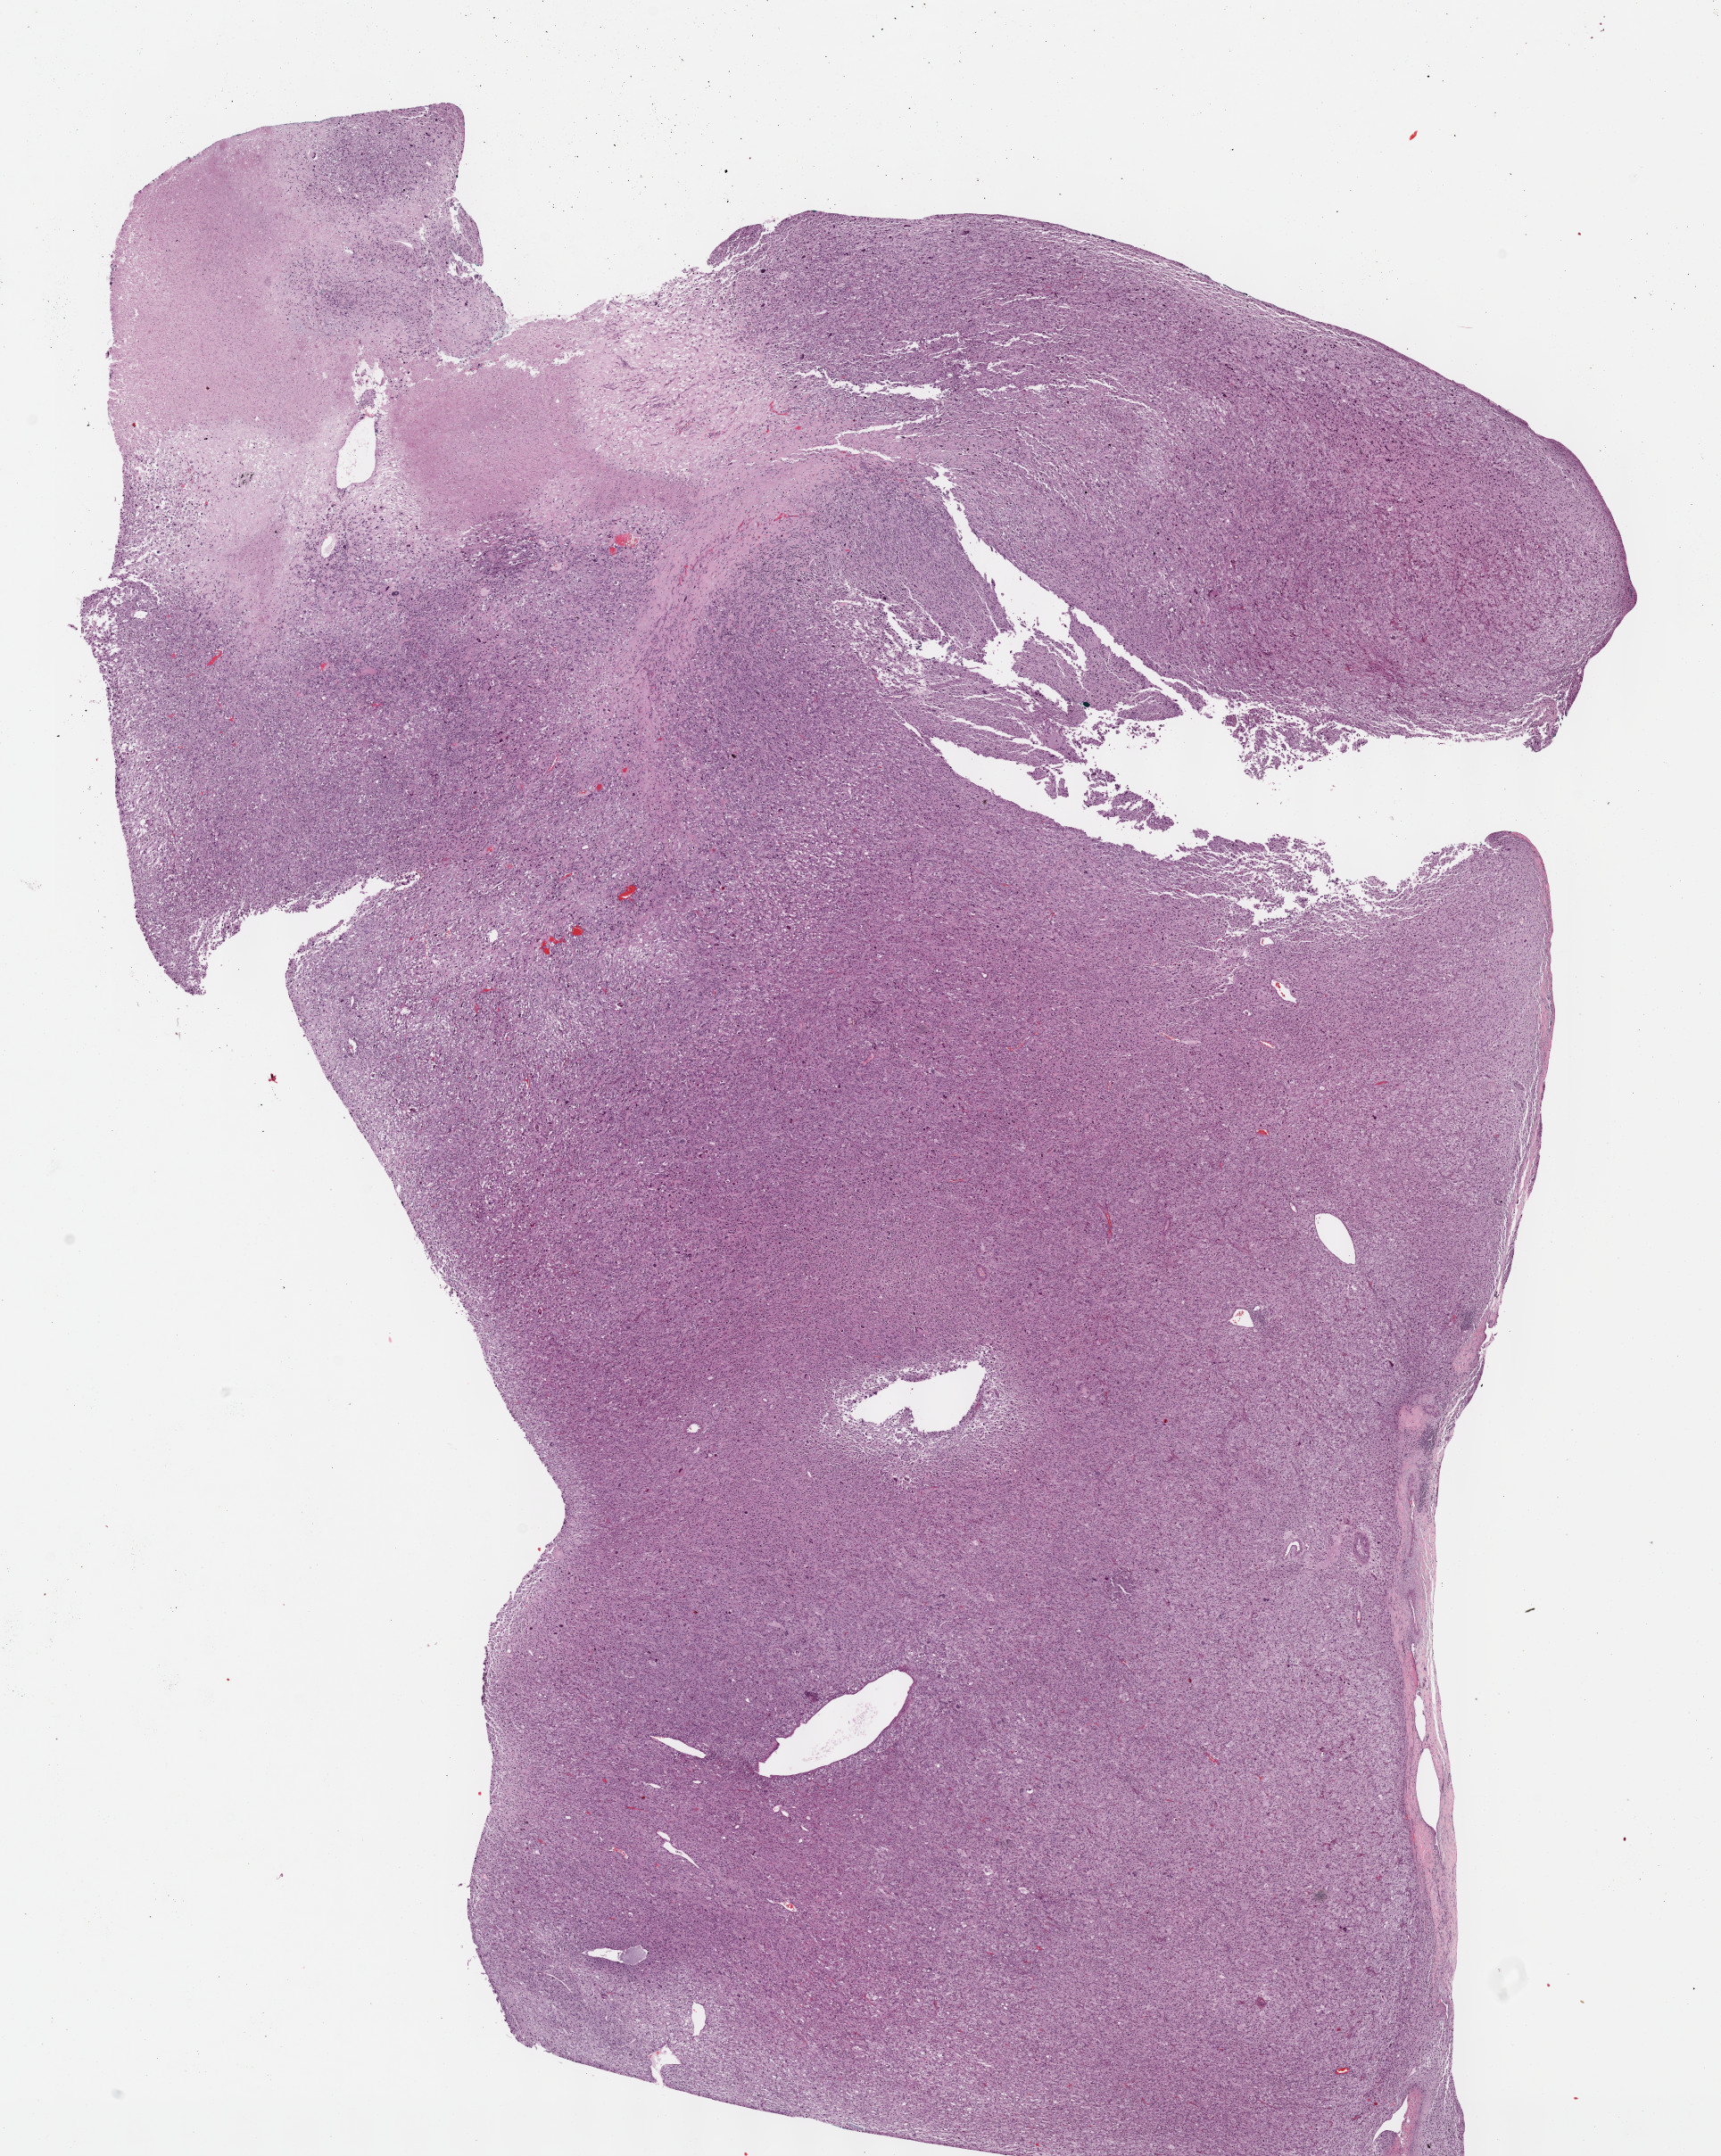
Whole-slide histology image, Hematoxylin and eosin (H&E) stained, low-resolution overview of the scanned area, about 15.6 x 19.5 mm (slide scanned at 40x), formalin-fixed paraffin-embedded (FFPE) diagnostic section, primary tumour sample from the connective, subcutaneous and other soft tissues. Patient: male, age at initial diagnosis 60 years.
- histologic diagnosis: Undifferentiated sarcoma (connective, subcutaneous and other soft tissues of lower limb and hip)